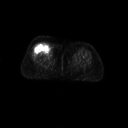
FDG PET of an extremity soft-tissue mass (from a PET/CT study), one axial slice. Position 27 of 267 along the scan axis. 128 × 128 image matrix, field of view 700 × 700 mm. Female patient, age 56 years. Case-level facts recorded for this patient, not image findings: histological type: malignant solitary fibrous tumor; grade: intermediate; site of the primary tumour: right thigh.
Annotated regions visible in this slice (expert contour drawn on MRI and transferred to this co-registered scan by the dataset authors):
- gross tumour volume including surrounding oedema: box from (x=36, y=41) to (x=55, y=56) px
- gross tumour volume (mass): (x=36, y=42)–(x=53, y=55)